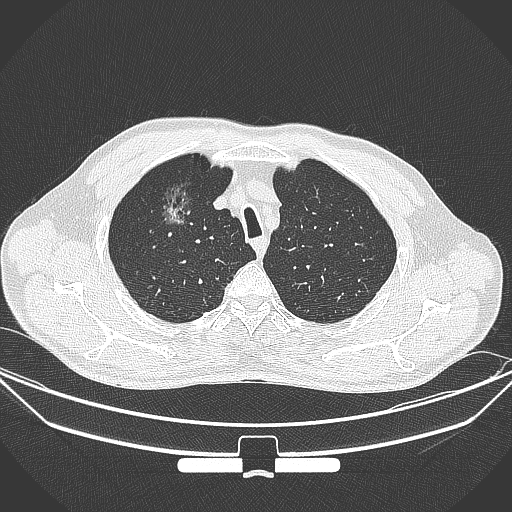
Chest CT, one axial slice. Position 285 of 355 along the scan axis. 120 kVp. Lung window (W 1500 / L -600 HU). 1 mm slice thickness. 512 × 512 image matrix. Male patient, age 67 years. Case-level facts recorded for this patient, not image findings: clinical TNM (as recorded): T1c N0 M0.
Outlined on this slice (bounding box drawn by a radiologist):
- lung tumour (recorded histology: adenocarcinoma): box from (x=154, y=179) to (x=202, y=239) px